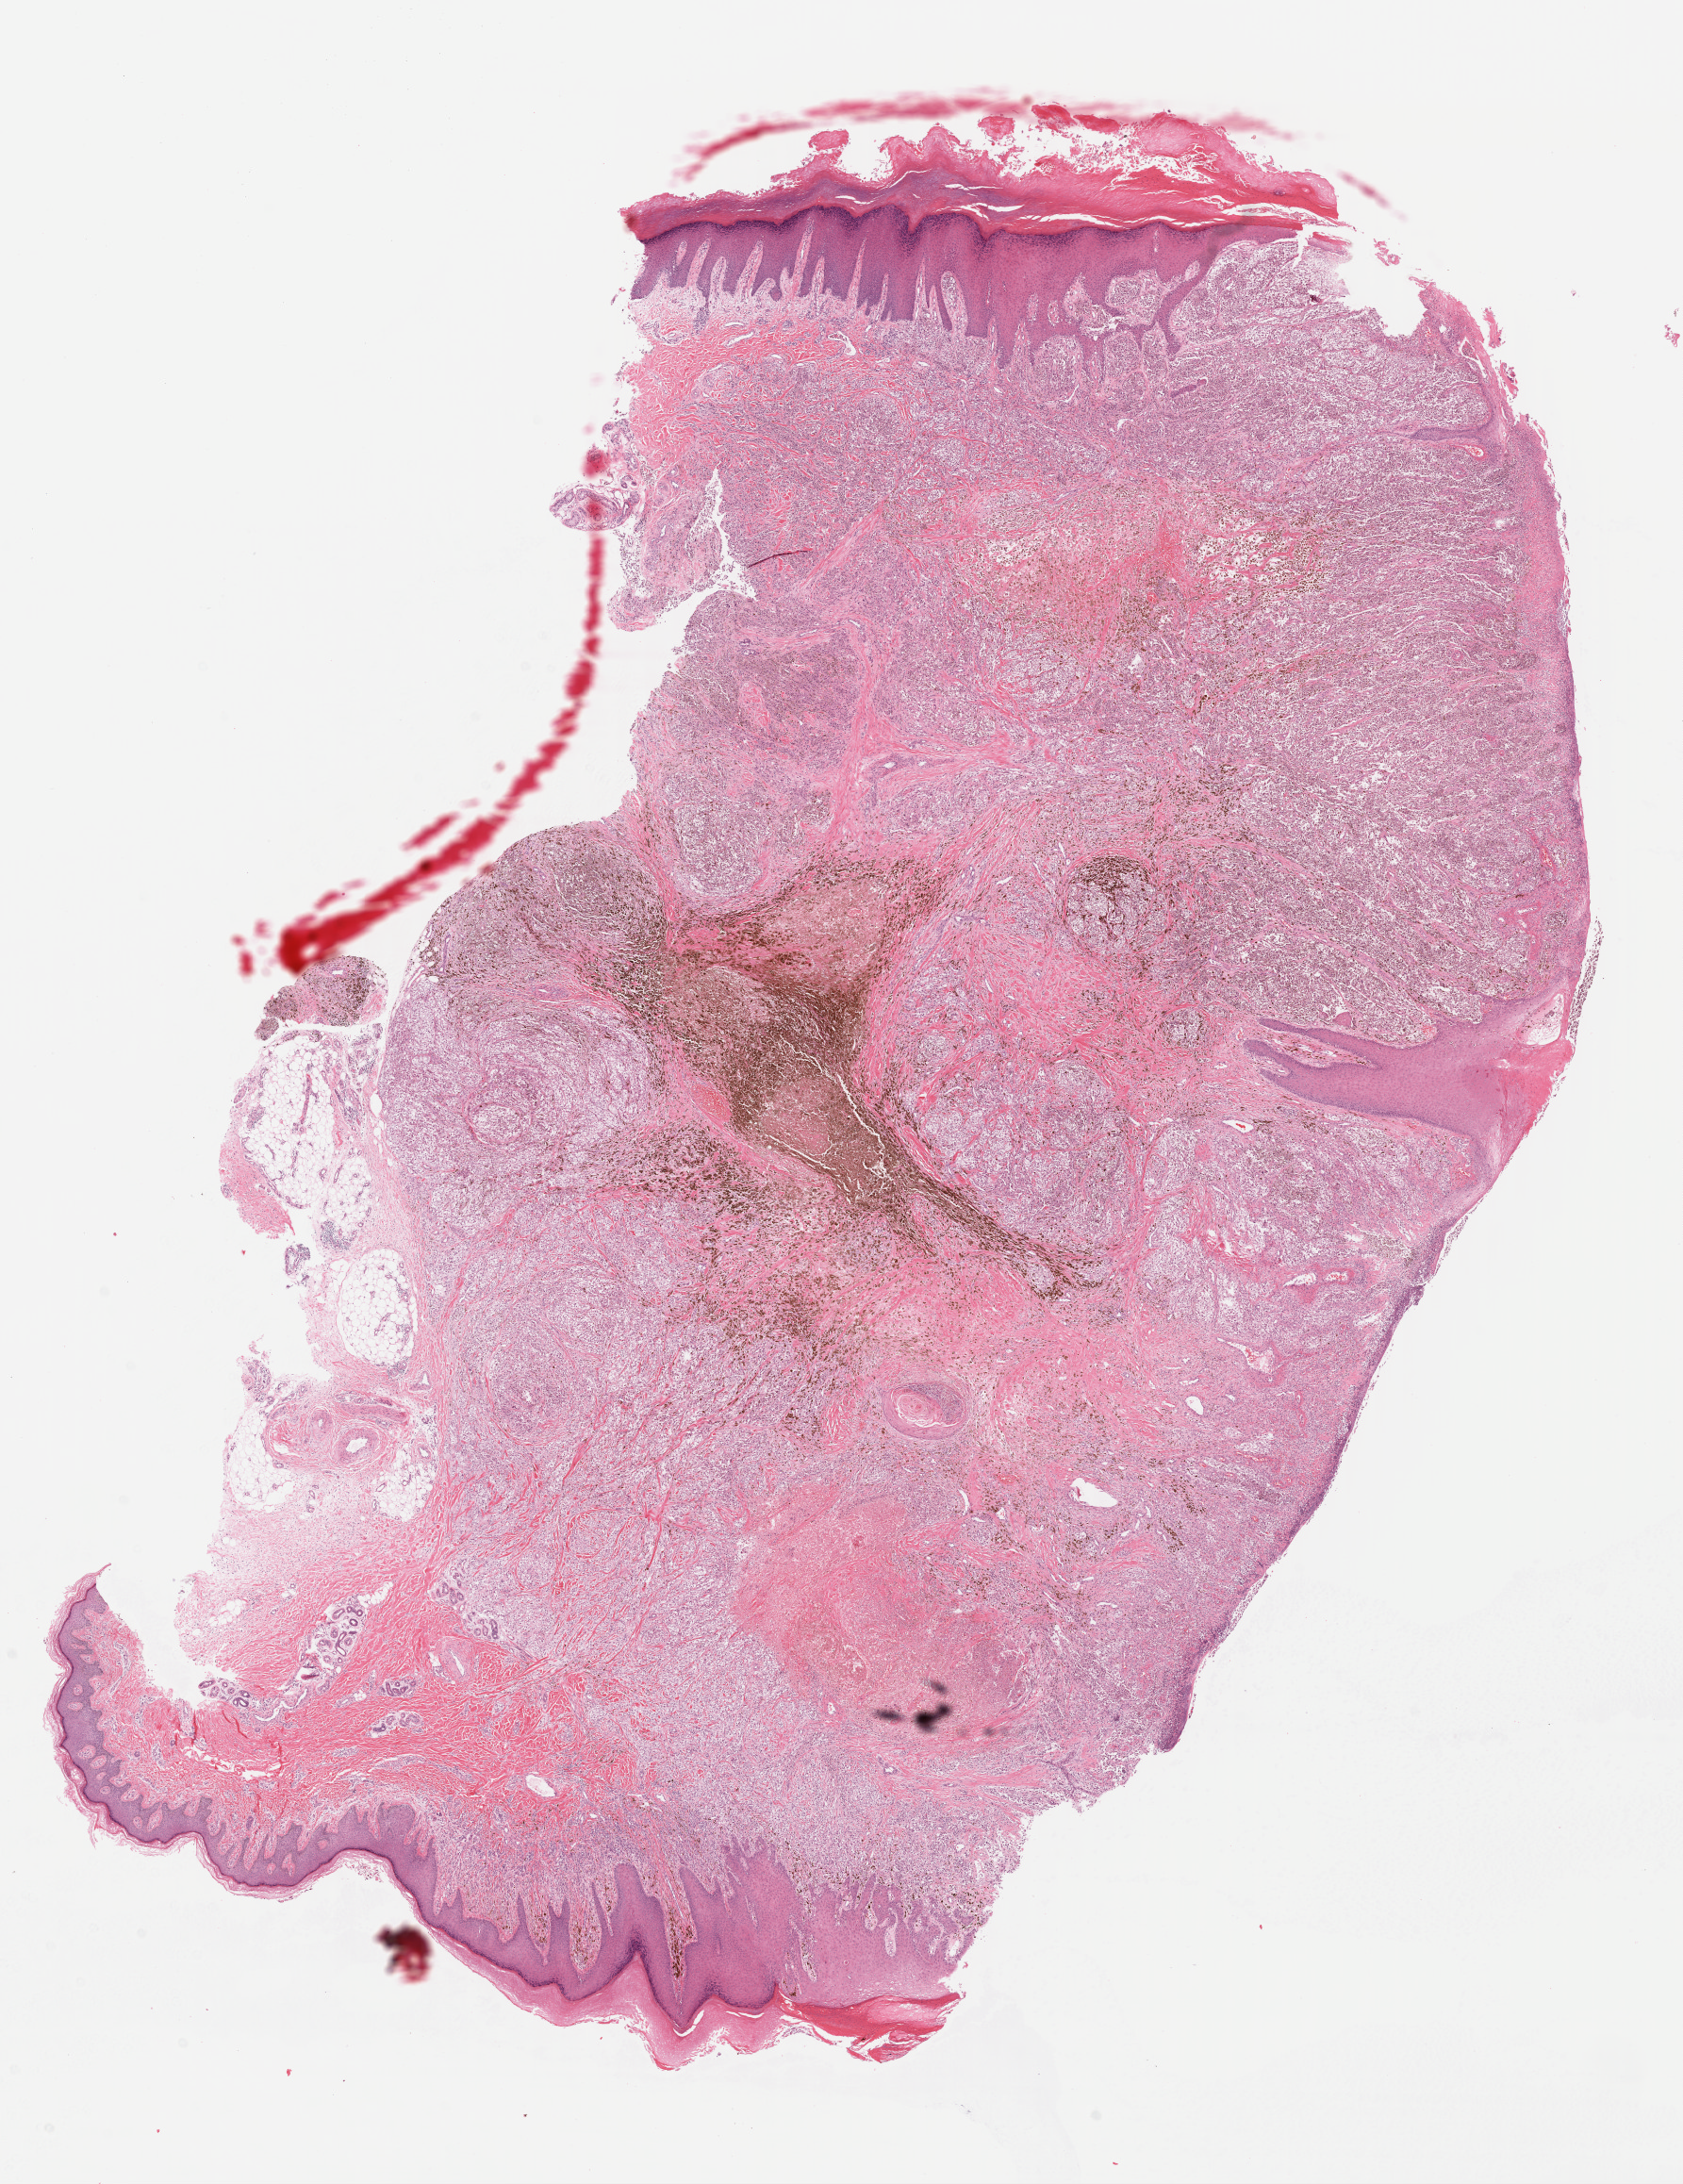
H&E whole-slide image, a low-resolution overview of the entire scanned area, about 14.0 x 18.2 mm. FFPE section. Primary tumour sample from the skin. Female, age 78 years at initial diagnosis.
Diagnosis: Nodular melanoma.